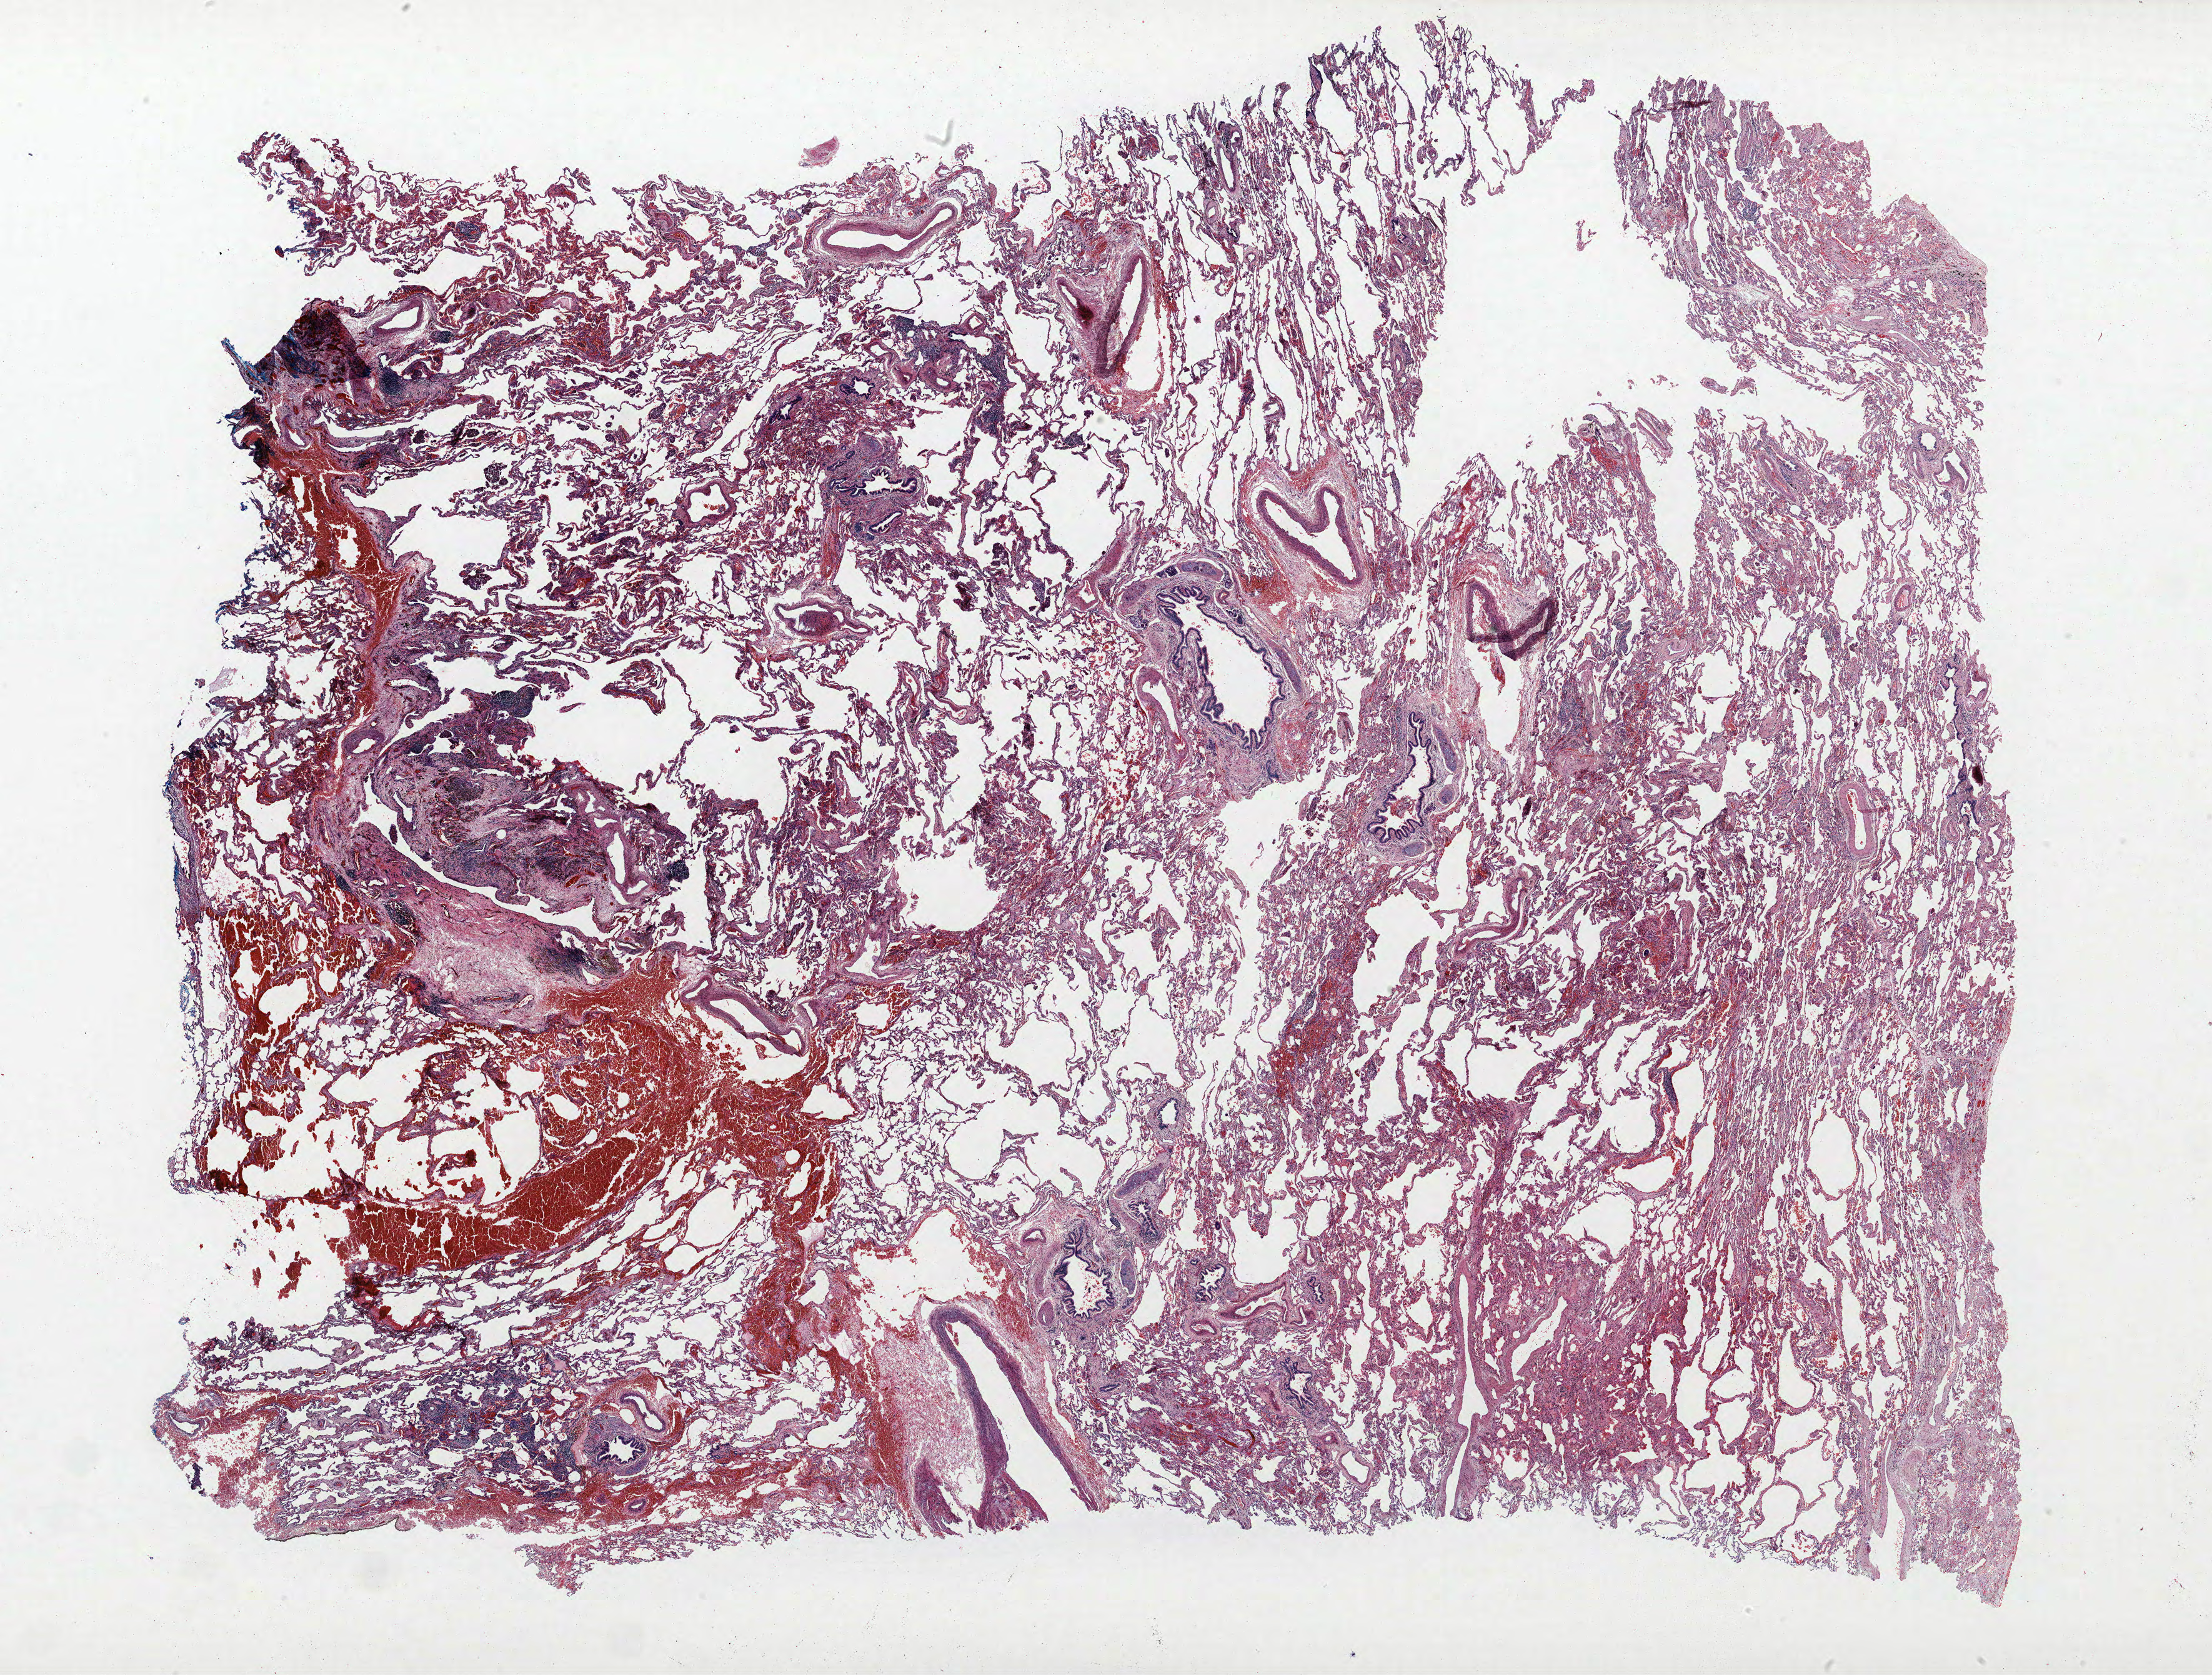
Whole-slide histology image, H&E, low-resolution overview of the scanned area, about 28.3 x 21.4 mm (slide scanned at 40x). Formalin-fixed paraffin-embedded (FFPE) section. Lung tissue. Female, age 59 at enrolment. Current smoker at enrolment. Grade: moderately differentiated (G2).
* primary tumour location (clinical record): right middle lobe
* tumour size (pathology): 11 mm
* stage (AJCC 6th edition): IA
* ICD-O-3 topography: middle lobe of lung (C34.2)
* participant's lung-cancer diagnosis: Adenocarcinoma, NOS
* note: participant had 2 primary lung cancers recorded; fields above describe the first